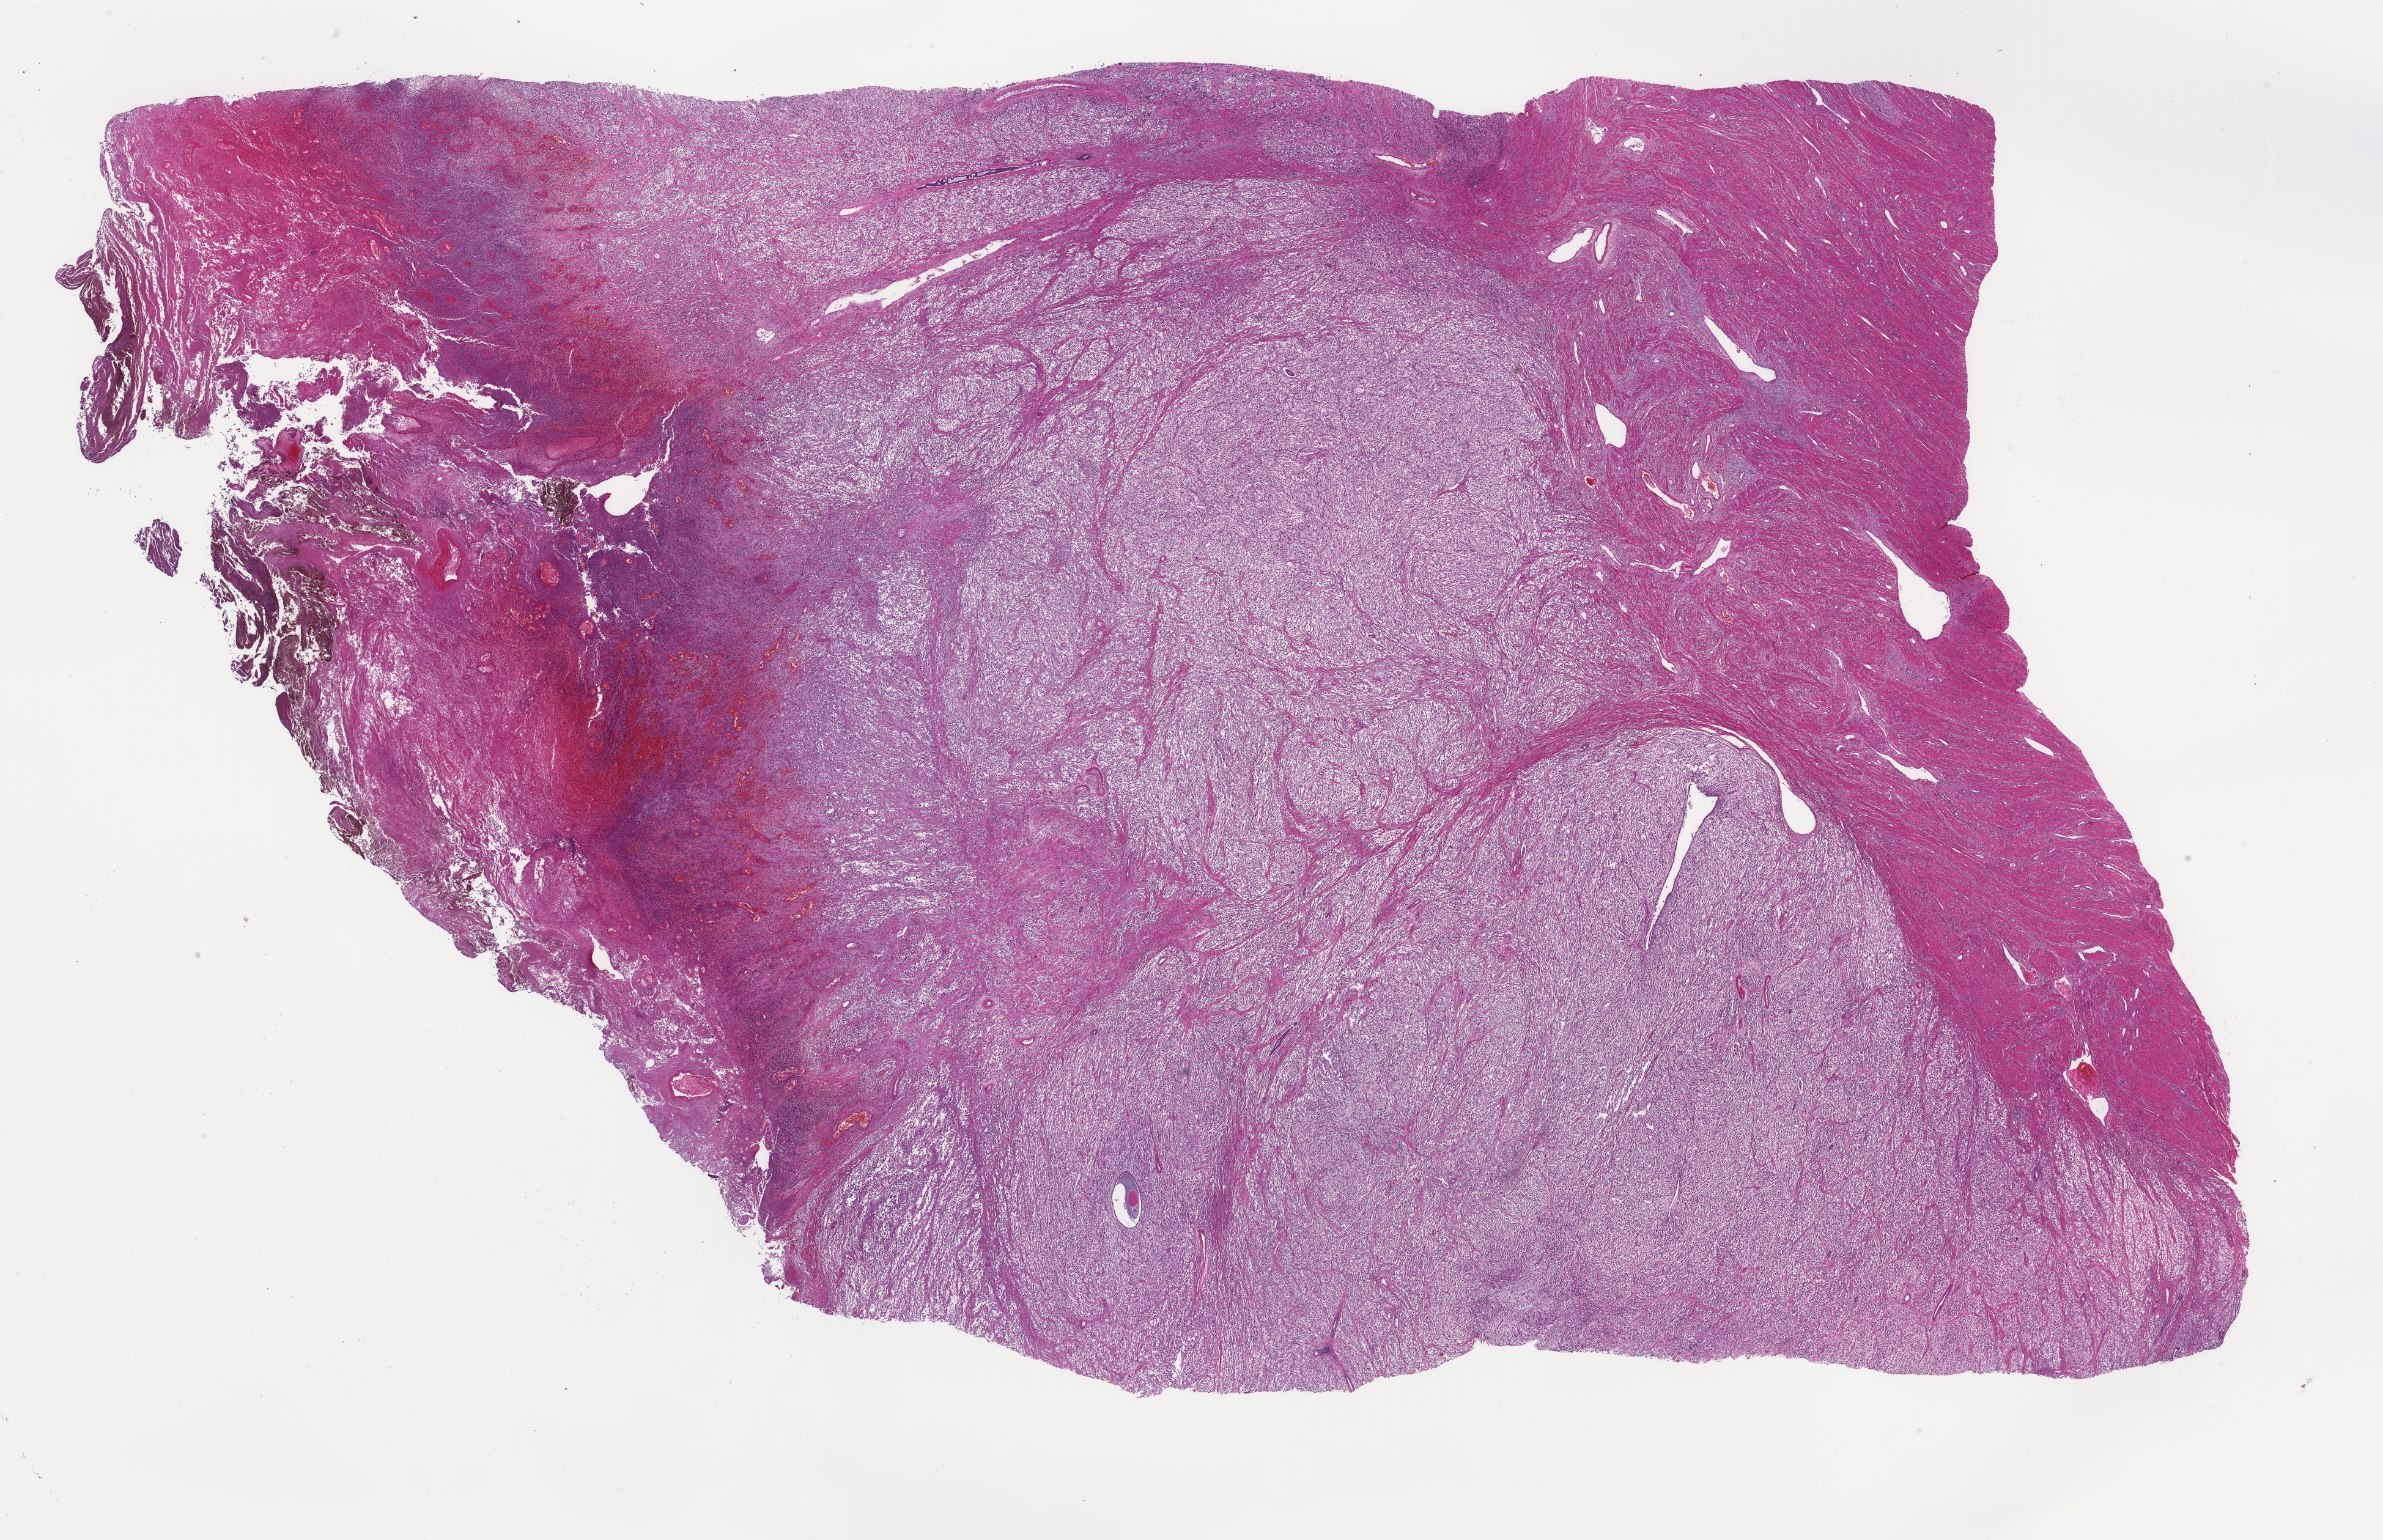
Digitized Hematoxylin and eosin (H&E) stained tissue section (whole slide), low-resolution overview of the scanned area, about 30.9 x 20.0 mm (acquisition: 40x scan); formalin-fixed paraffin-embedded (FFPE) diagnostic section; sample: primary tumour, uterus. Female, age 60 years at initial diagnosis.
Histologic diagnosis: Carcinosarcoma, NOS. FIGO stage: IVB.